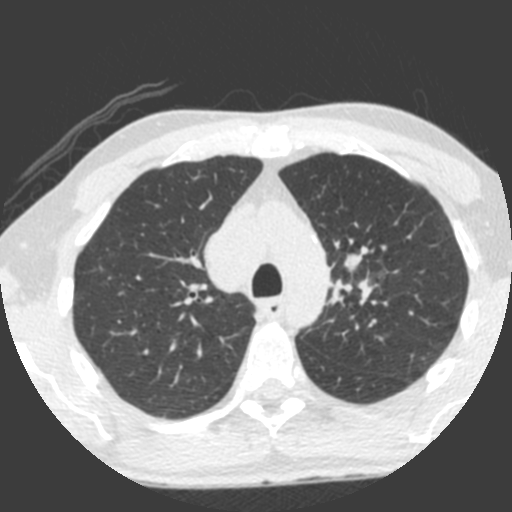
Low-dose screening chest CT, one axial slice. Slice 157 of 212 in the series (ordered by position). 120 kVp. Lung window (W 1500 / L -600 HU). 2 mm slice thickness. 512 × 512 image matrix, field of view 315 × 315 mm.
Annotated regions visible in this slice (outlined manually by an expert reader):
- lesion 1 (tumor, upper lobe of left lung): bounding box (x1, y1, x2, y2) in pixels: (342, 246, 368, 271)